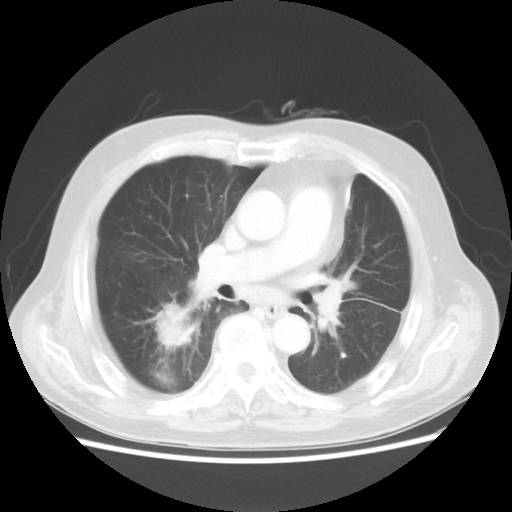
Chest CT, one axial slice. Slice 21 of 44 in the series (ordered by position). Reconstruction kernel STANDARD. Lung window (W 1500 / L -600 HU). 5 mm slice thickness. 512 × 512 image matrix. Patient: male, 83 years. From the clinical record (not read from this slice): clinical TNM (as recorded): T2 N3 M0.
Annotated regions visible in this slice (bounding box drawn by a radiologist):
- lung tumour (recorded histology: adenocarcinoma): box from (x=140, y=298) to (x=192, y=361) px